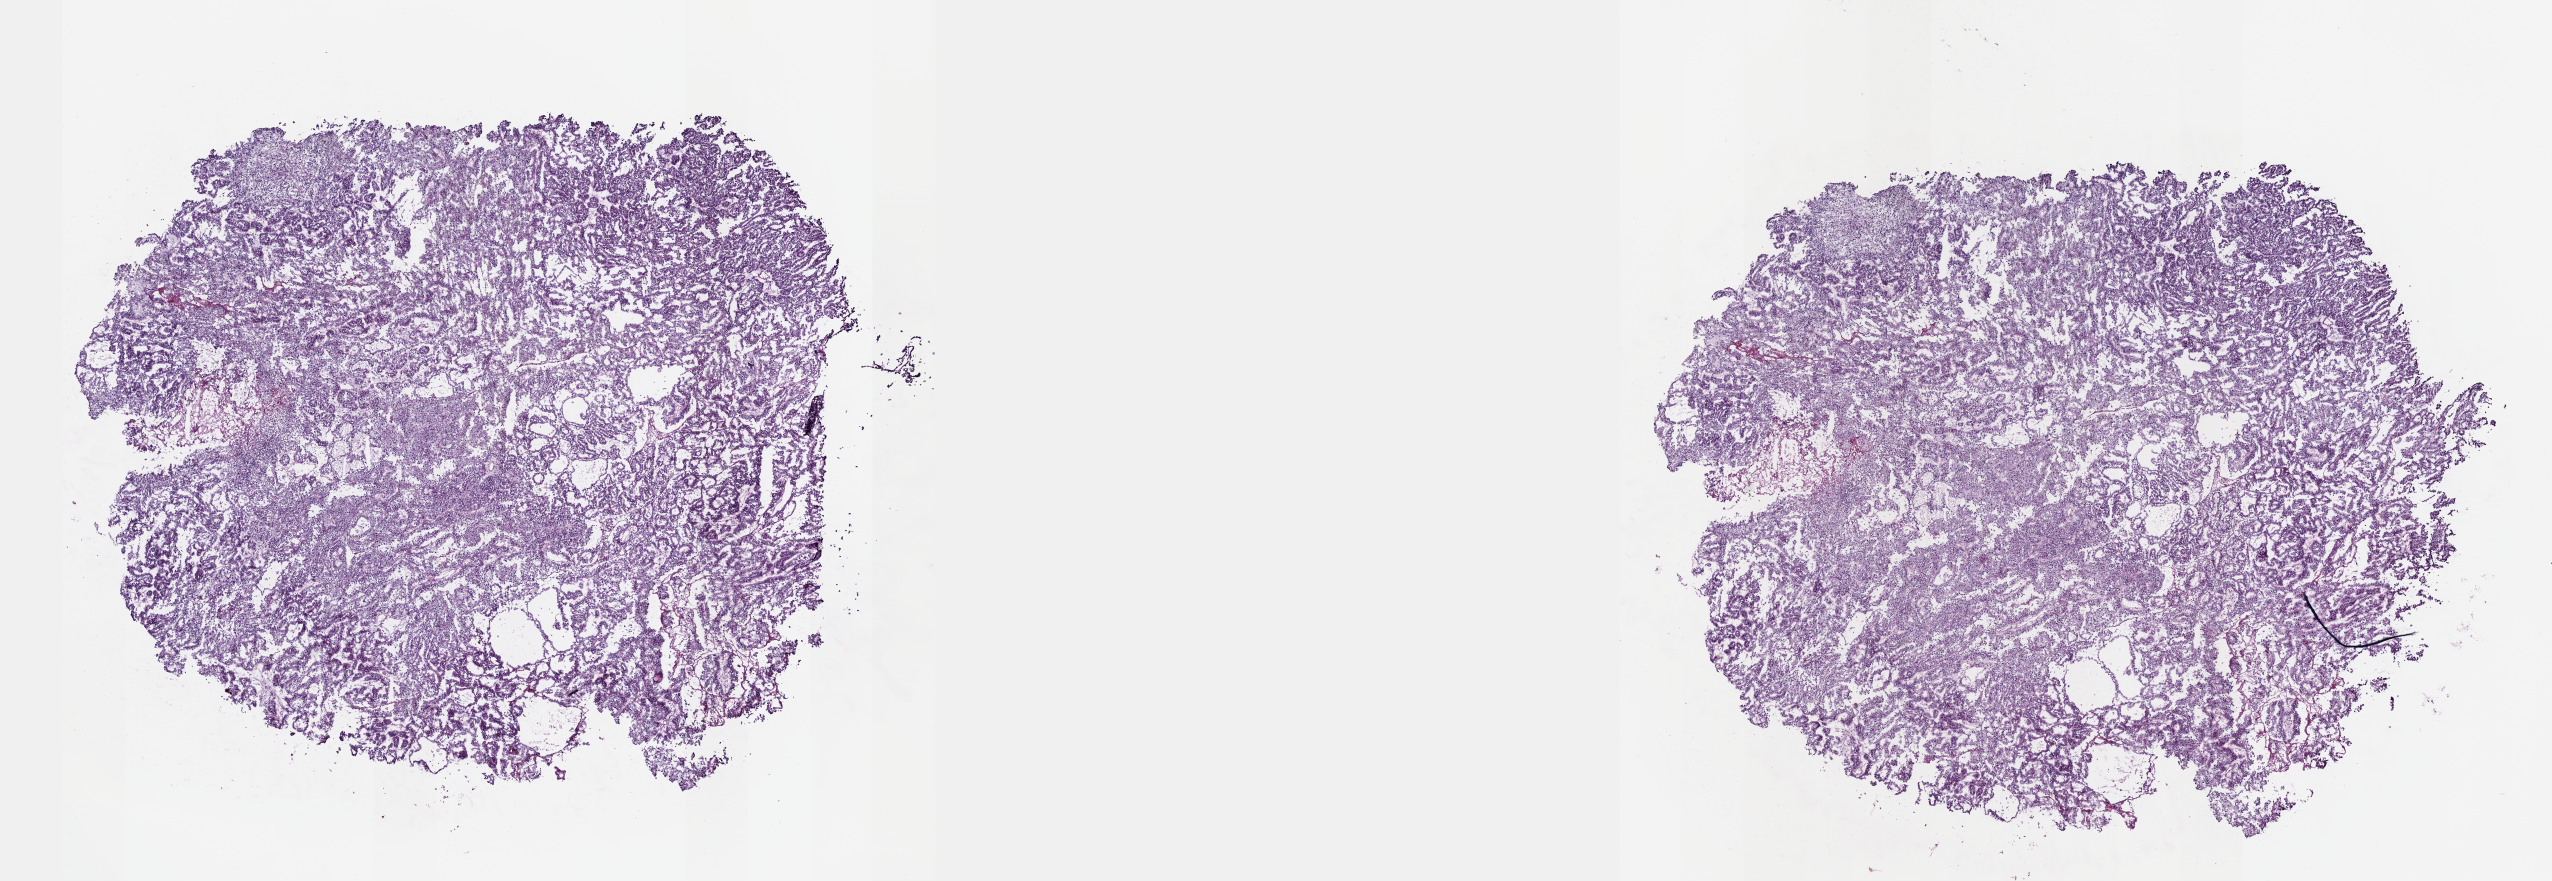
H&E-stained whole-slide image, whole scanned area (about 20.6 x 7.1 mm, acquisition: 40x scan) shown as a low-resolution overview; frozen section from the top of the tissue portion; kidney, primary tumour sample. Patient: female, age at initial diagnosis 62 years. Slide review estimates, as recorded: tumour cells 90%, tumour nuclei 95%, normal cells 0%, stromal cells 10%, necrosis 0%. Inflammatory infiltration, as recorded: lymphocyte infiltration 0%, monocyte infiltration 0%, neutrophil infiltration 0%.
* diagnosis: Papillary adenocarcinoma, NOS
* laterality: left
* TNM: T2 NX MX
* AJCC pathologic stage: II (6th edition)